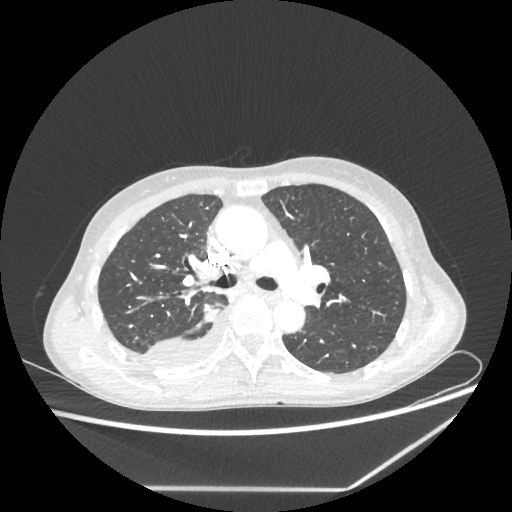
Chest CT, one axial slice. Position 148 of 237 along the scan axis. Reconstruction kernel STANDARD. Lung window (W 1500 / L -600 HU). 1.25 mm slice thickness. 512 × 512 image matrix. Female patient, age 59 years. From the clinical record (not read from this slice): clinical TNM (as recorded): T1c N1 M1.
Outlined on this slice (bounding box drawn by a radiologist):
- lung tumour (recorded histology: adenocarcinoma): bounding box (x1, y1, x2, y2) in pixels: (198, 303, 222, 326)